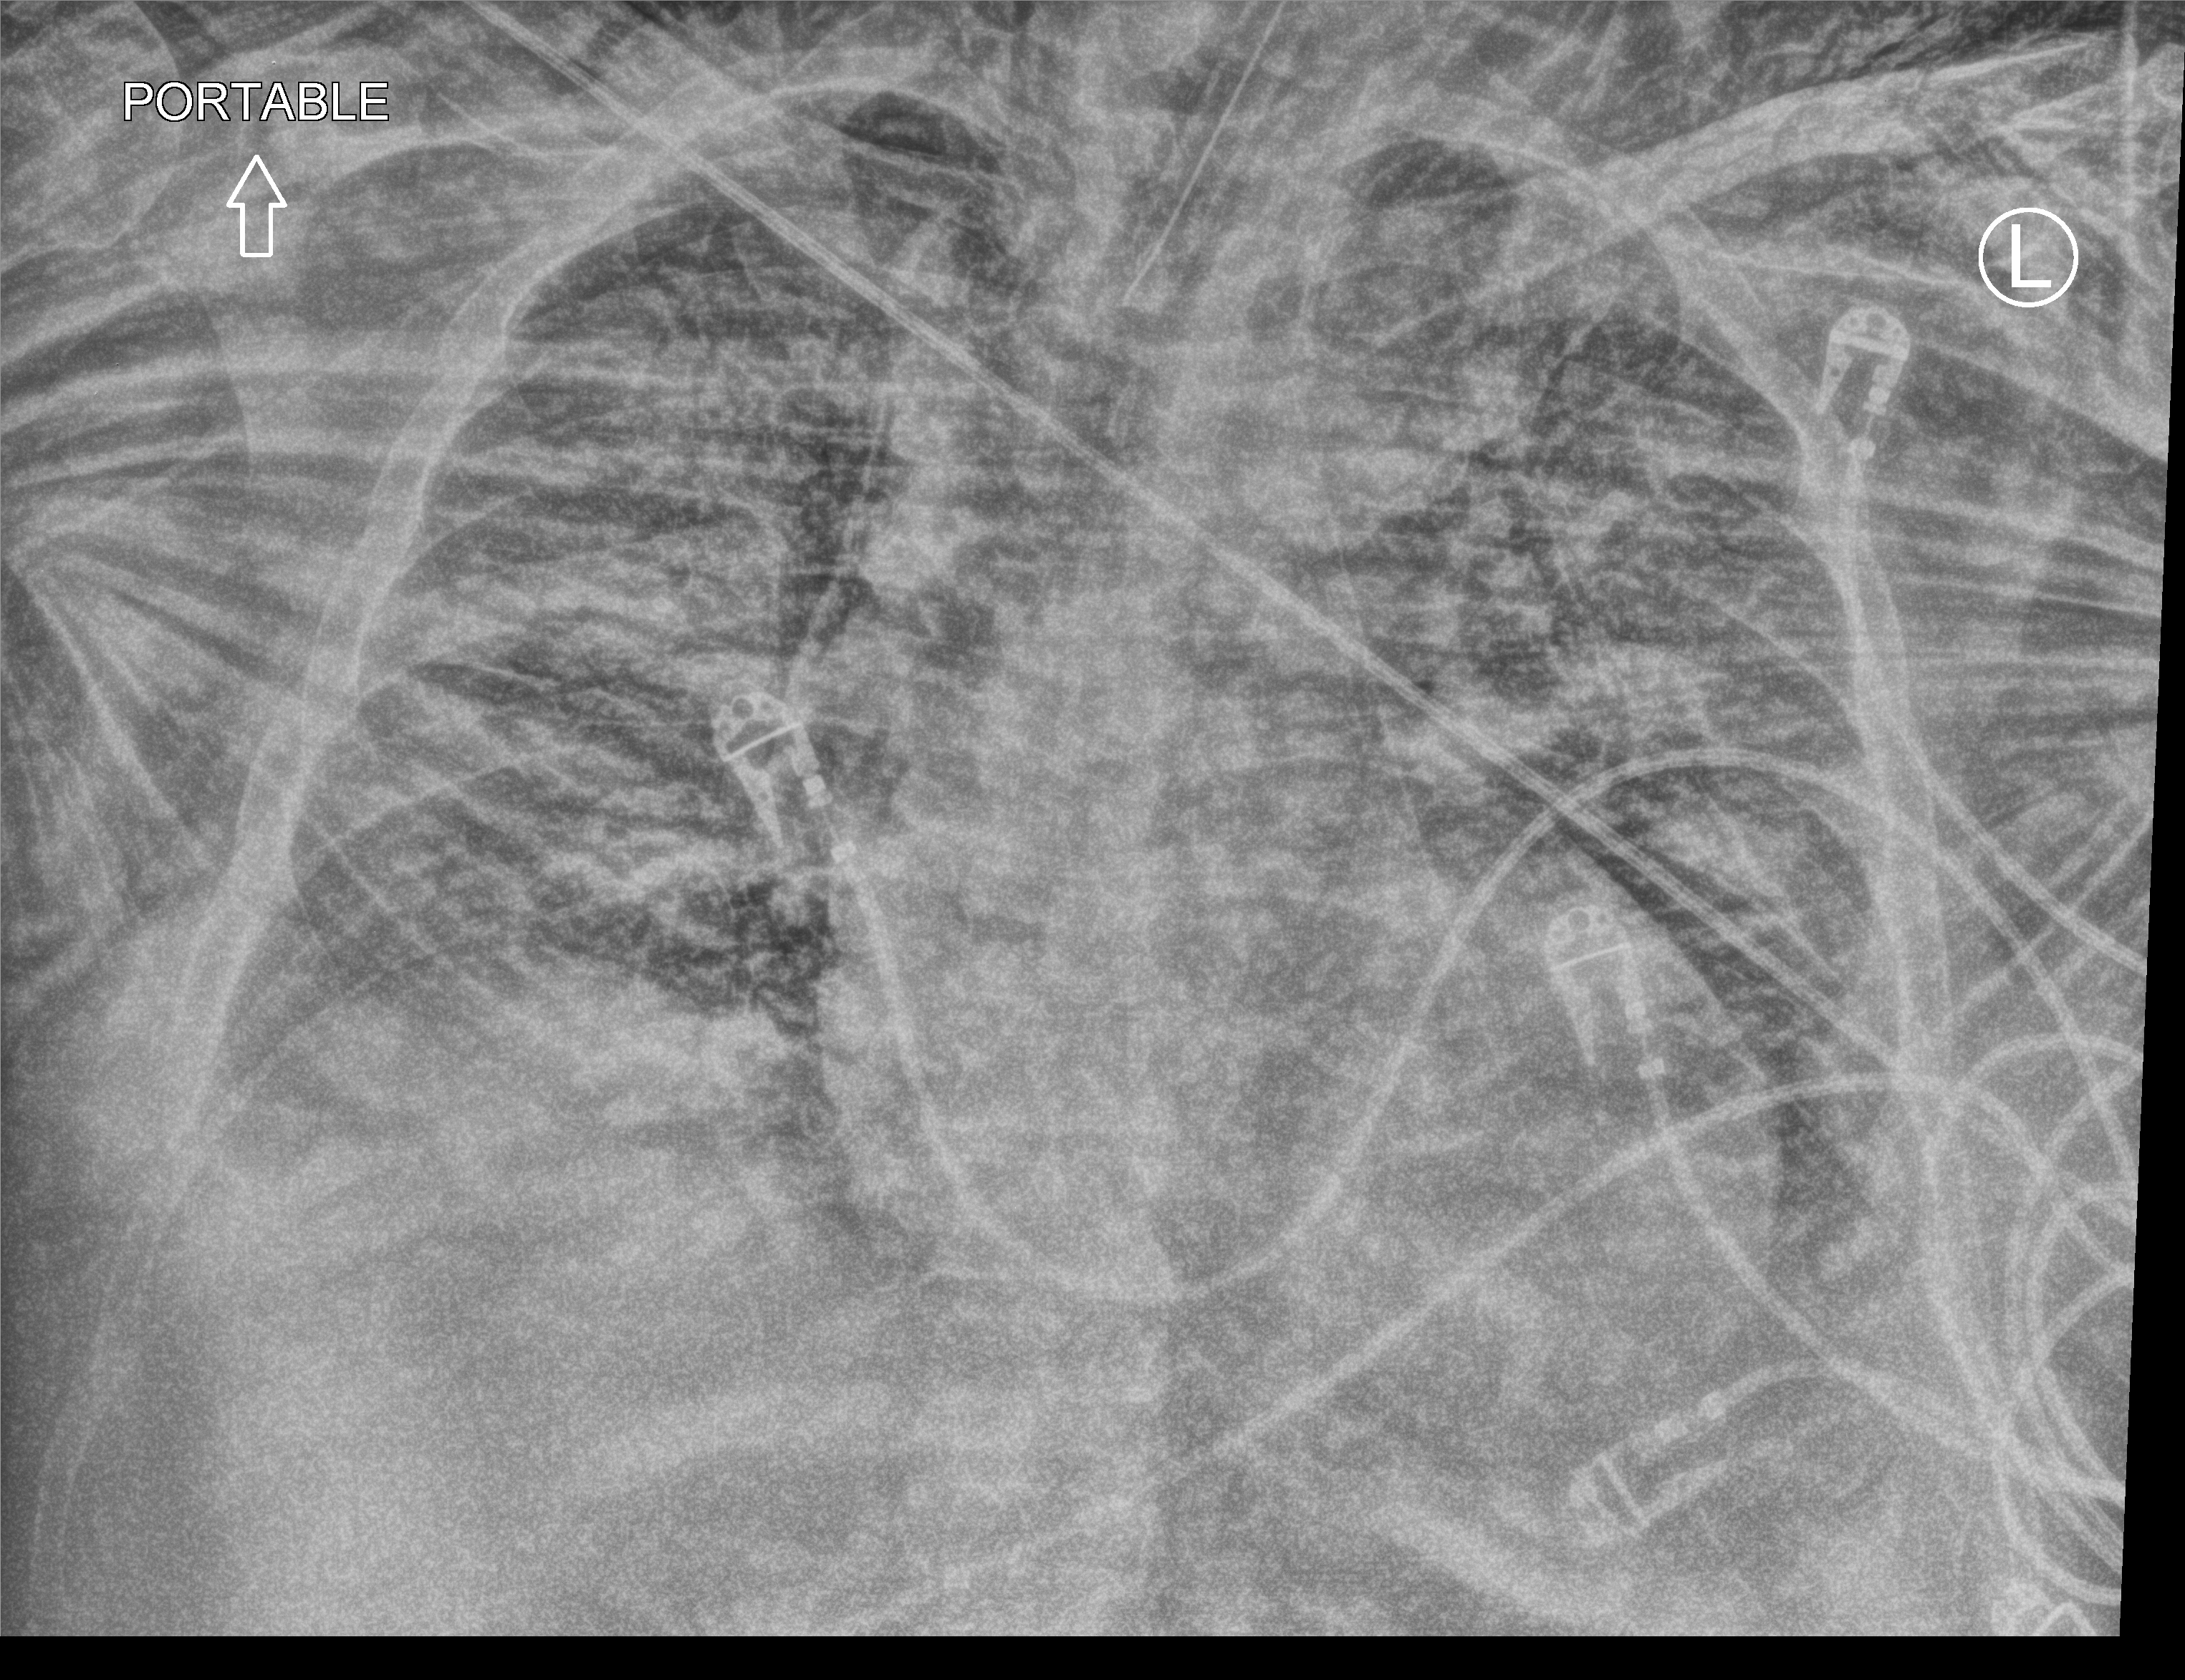
Portable chest radiograph; anteroposterior (AP) projection. Patient hospitalised with COVID-19, aged 18–59 years.
Admission-level facts for this patient (not findings on this image; timing relative to this image not recorded): COPD (admission record): no.